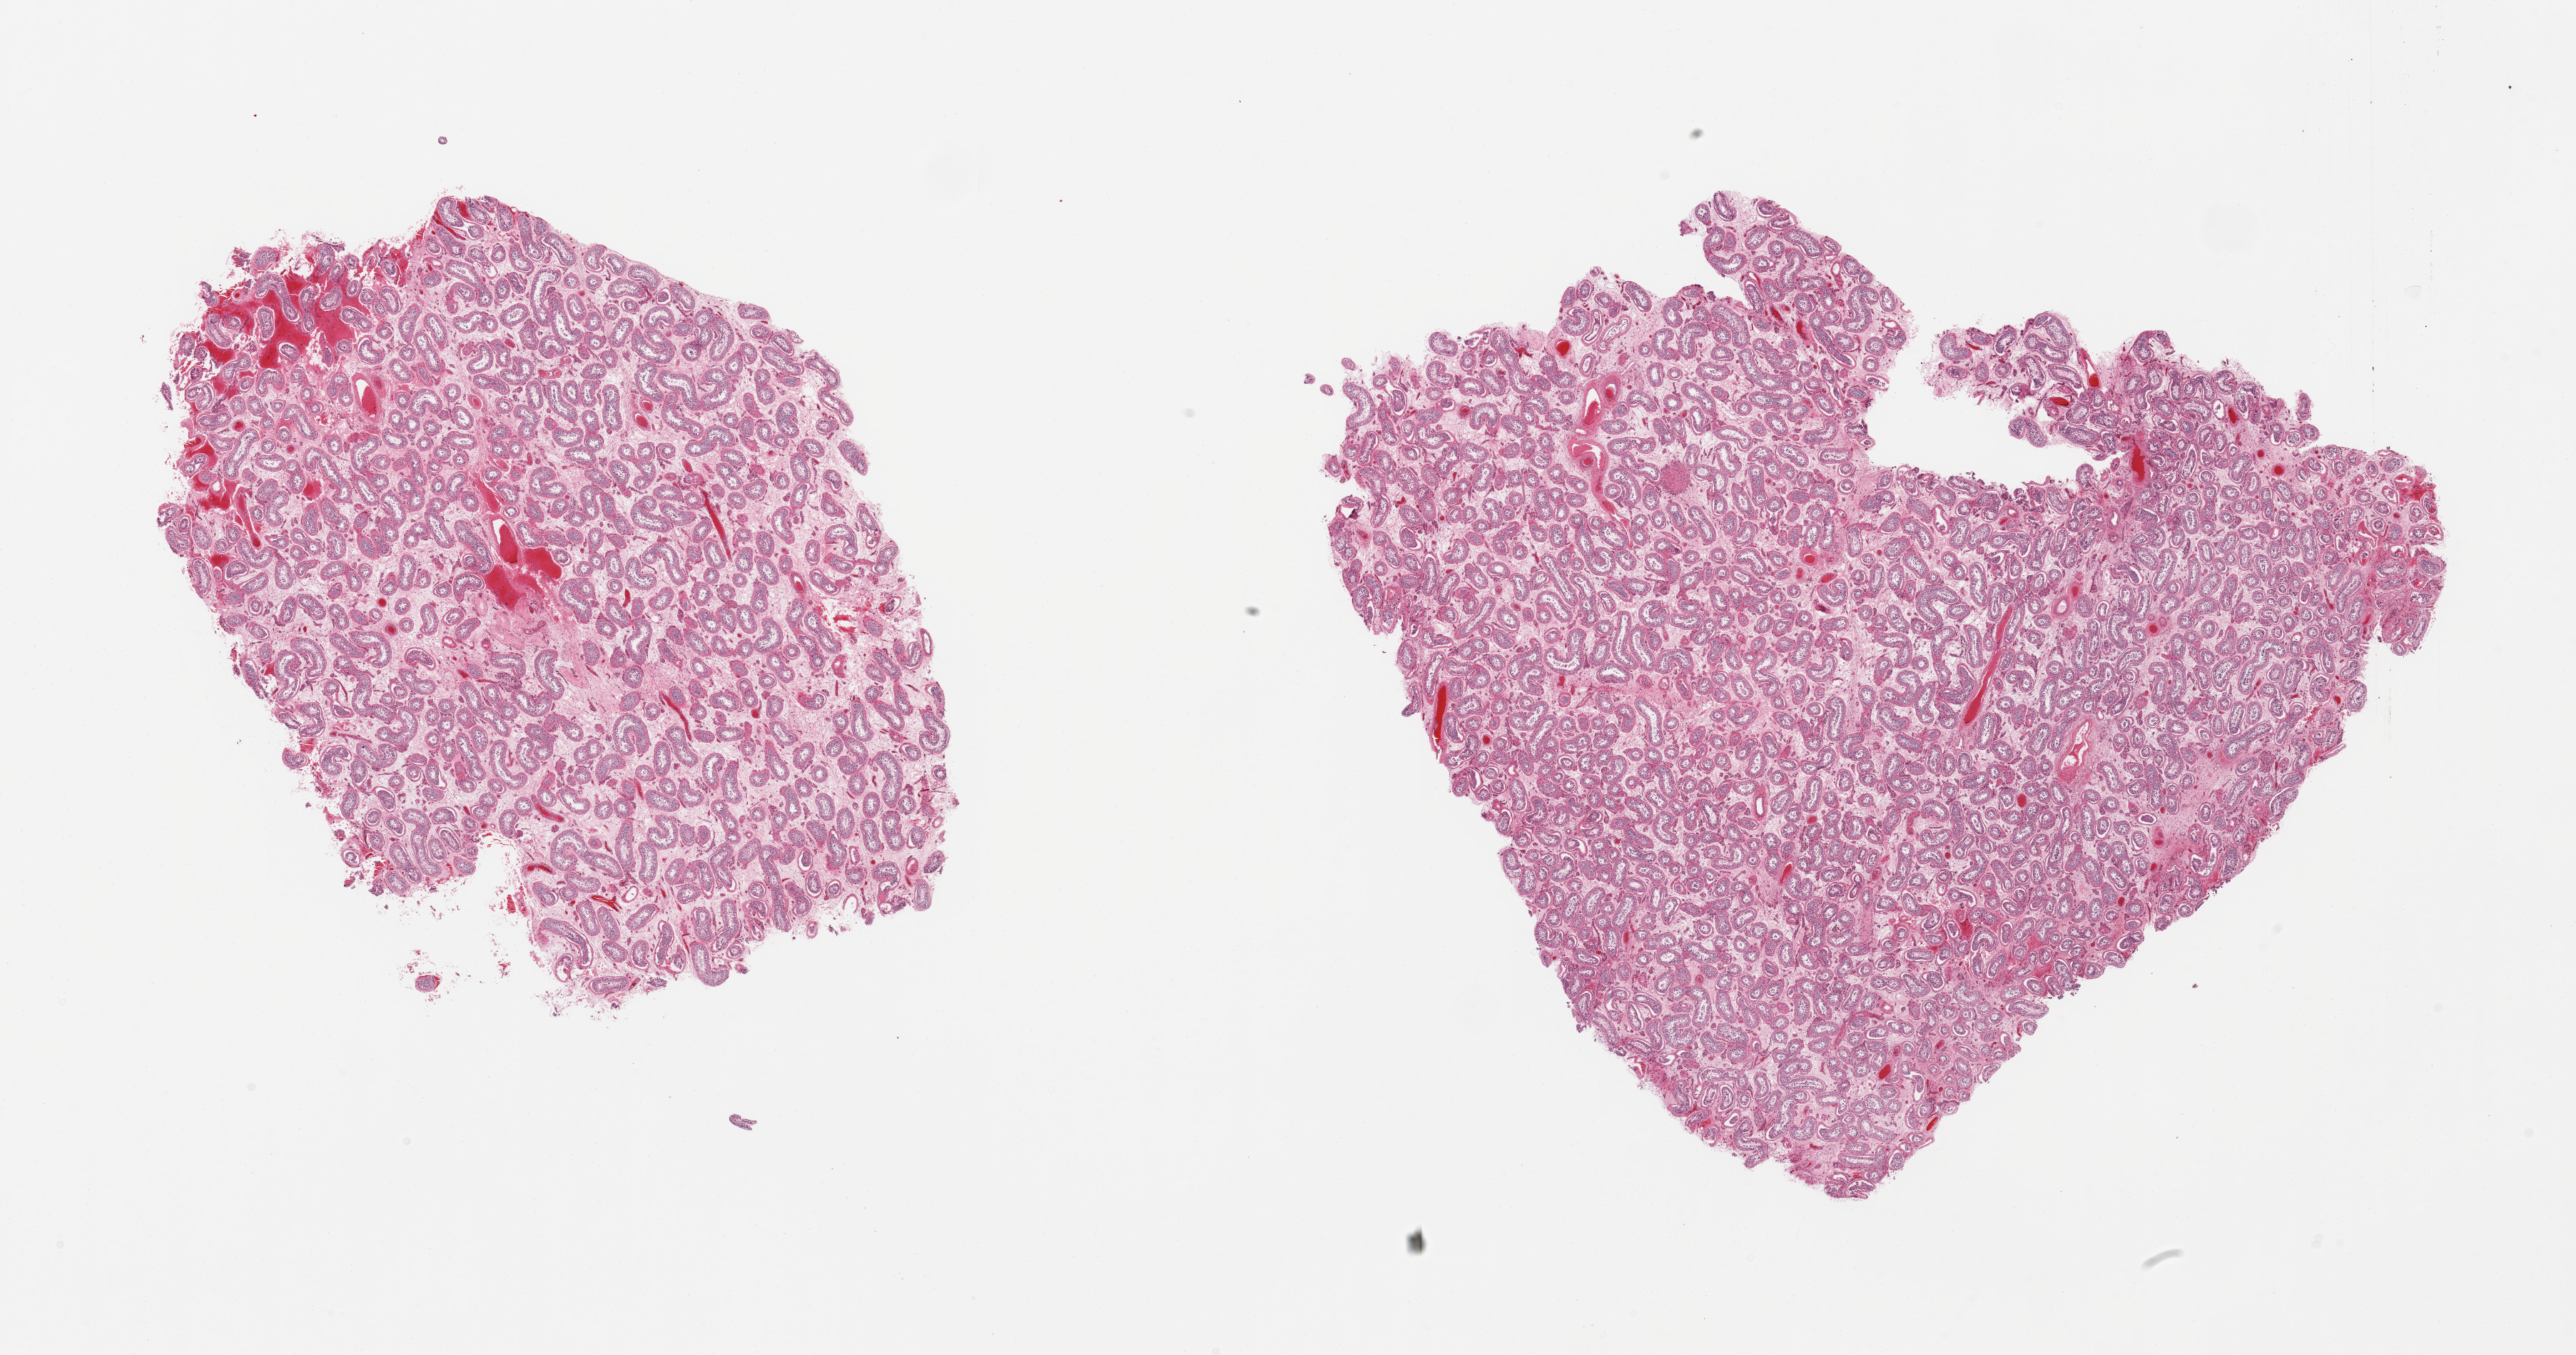
Haematoxylin and eosin whole-slide image, brightfield — shown as a low-resolution overview of the whole scanned area (about 28.5 x 15.0 mm), PAXgene-fixed, paraffin-embedded tissue, sampled site (target tissue): testis, tissue donor sample. Donor: male.
Reviewer comment on this tissue sample: 2 pieces, spermatogenesis appears notabely reduced, approaching 'Sertoili only.